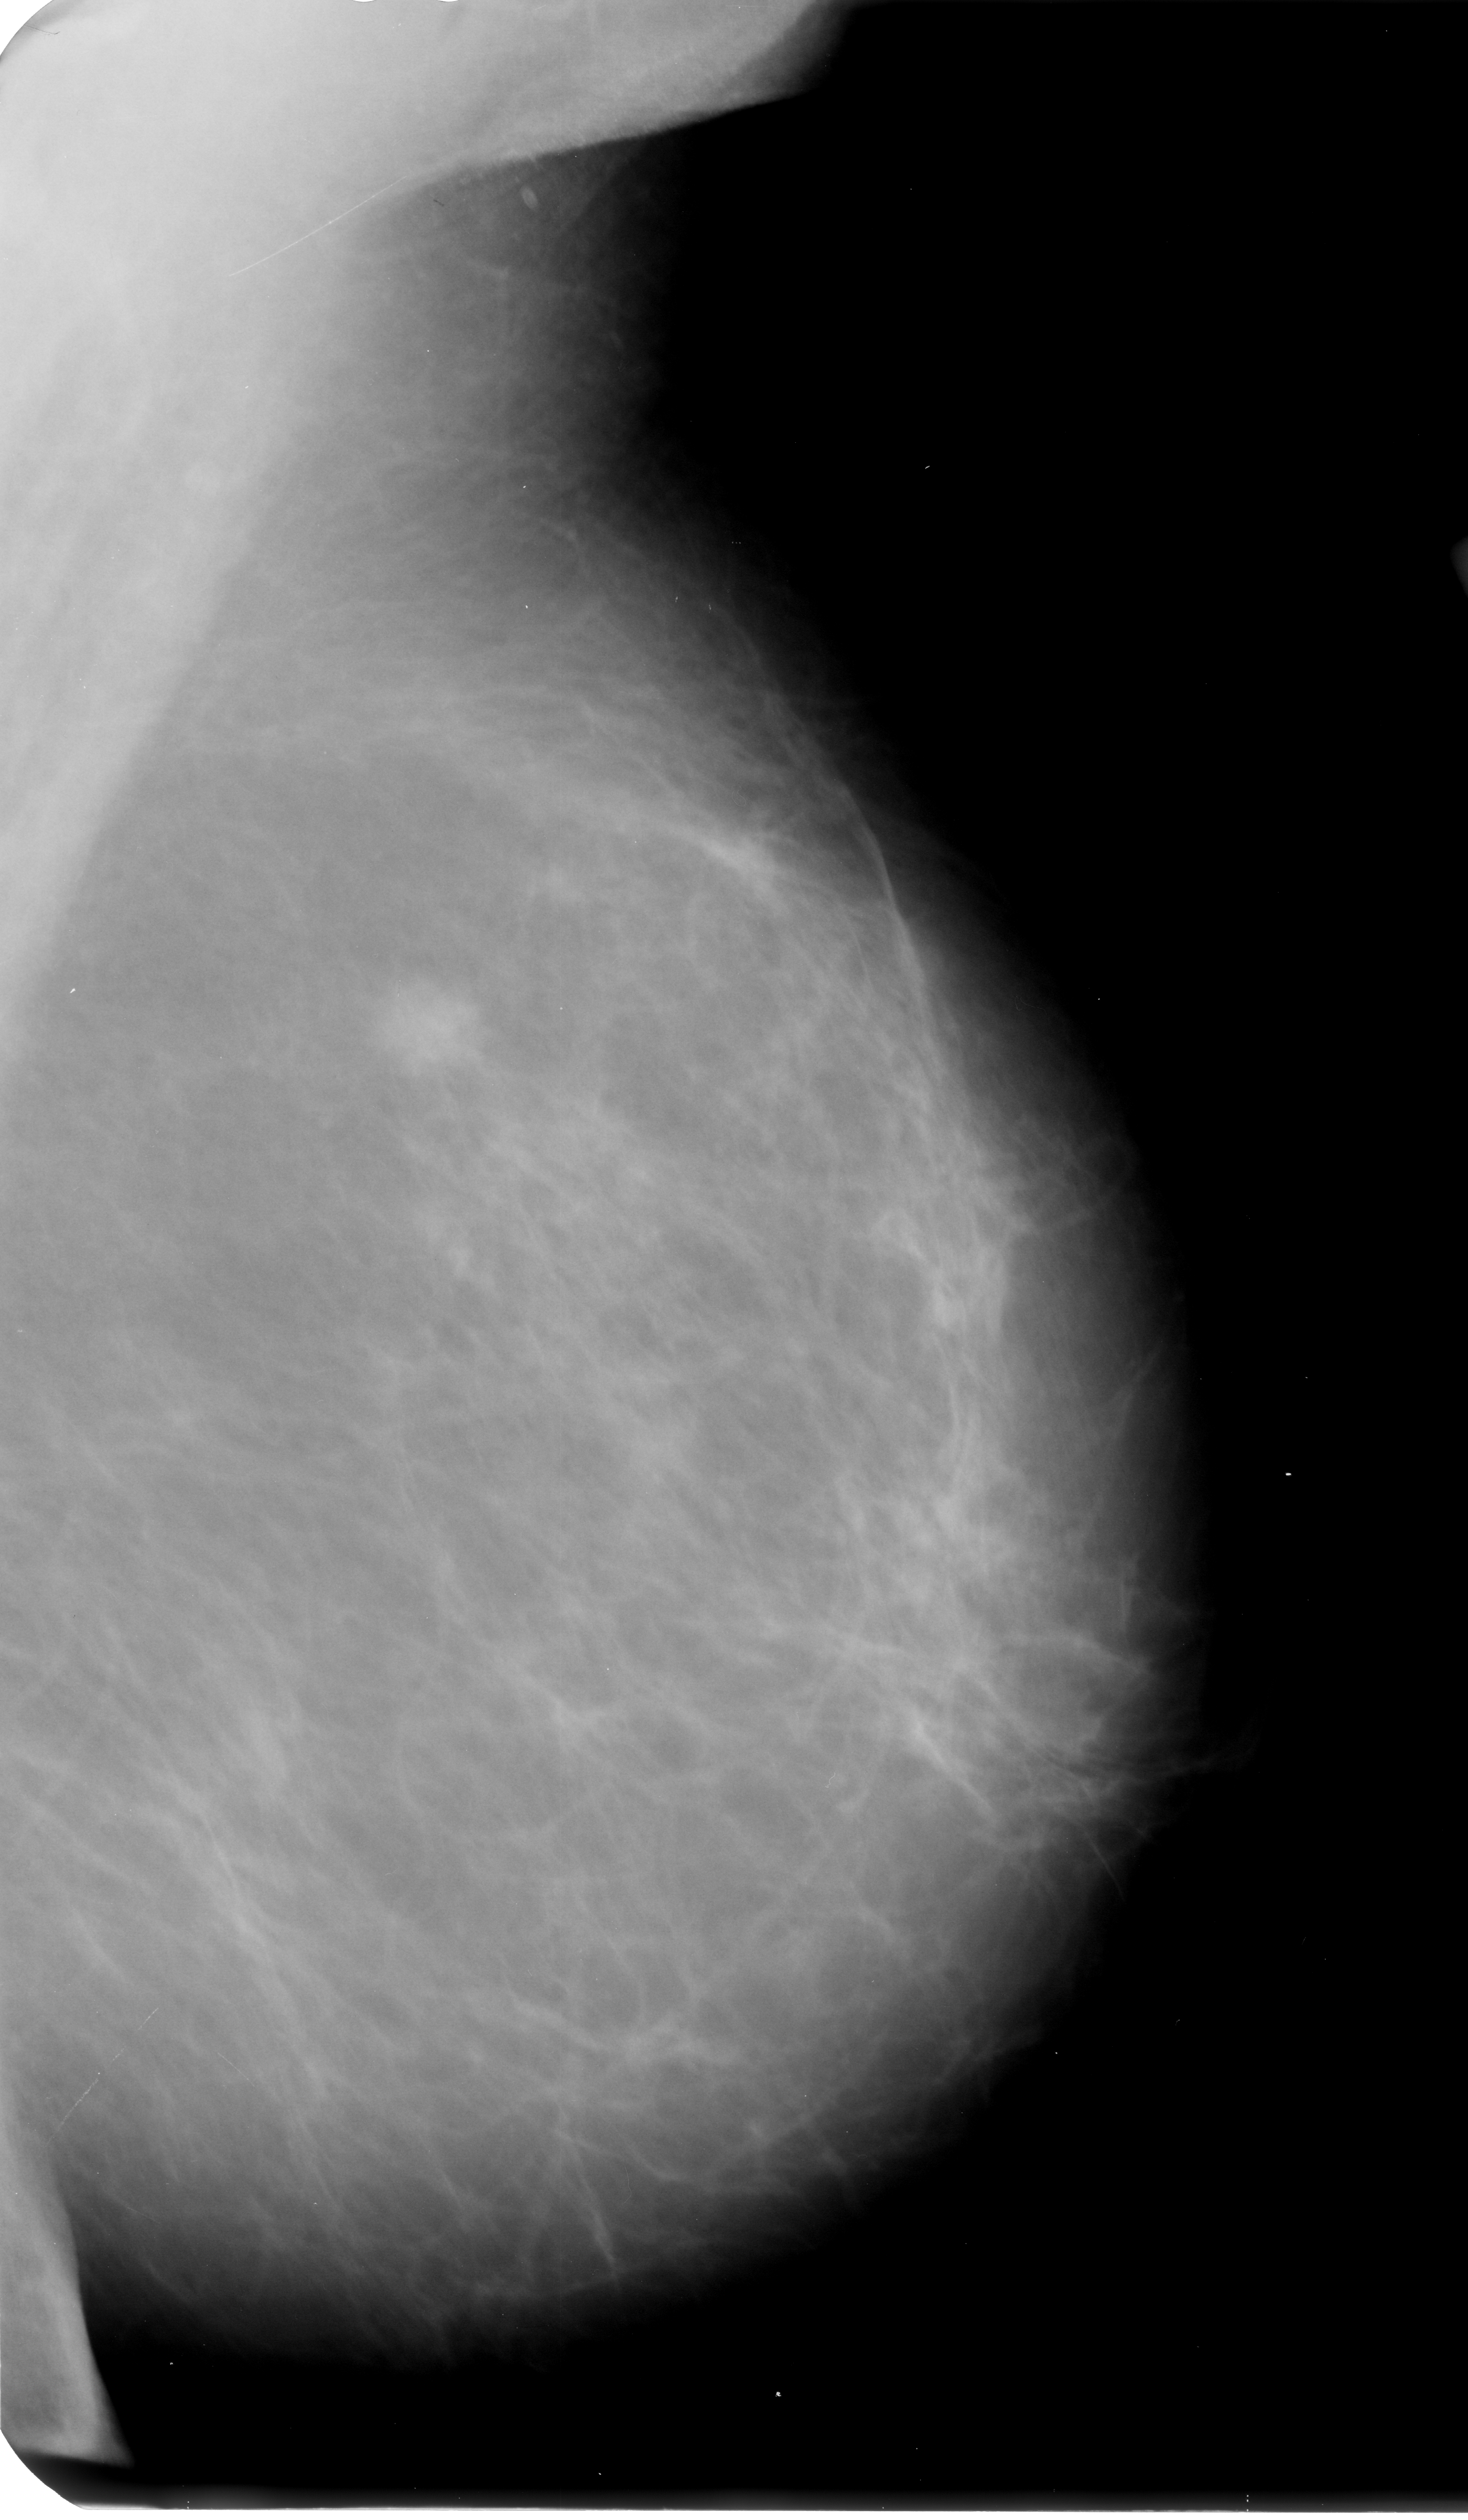
Mammogram (digitized film); left breast; mediolateral oblique (MLO) view; breast composition: scattered fibroglandular densities (BI-RADS density category 2 of 4).
Marked findings (only marked abnormalities are described; nothing is implied about the rest of the image): mass, shape irregular, margins spiculated; BI-RADS assessment category 4; pathology (as recorded): malignant.